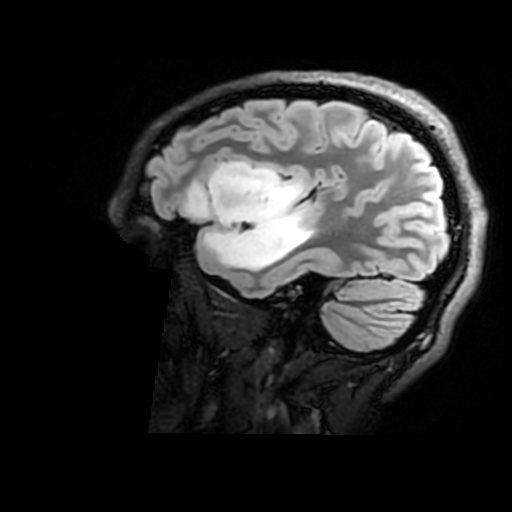
Brain MRI from a brain-tumour surgery series, one sagittal slice. Slice 129 of 176 in the series (ordered by position). T2 FLAIR. 512 × 512 image matrix, field of view 240 × 240 mm. From the clinical record (not read from this slice): histopathology: Astrocytoma; WHO grade: 2; IDH mutation: yes; tumour location: Right Insular.
Annotated regions visible in this slice (outlined manually by an expert reader):
- tumour: bounding box [x1, y1, x2, y2] px = [188, 161, 314, 272]